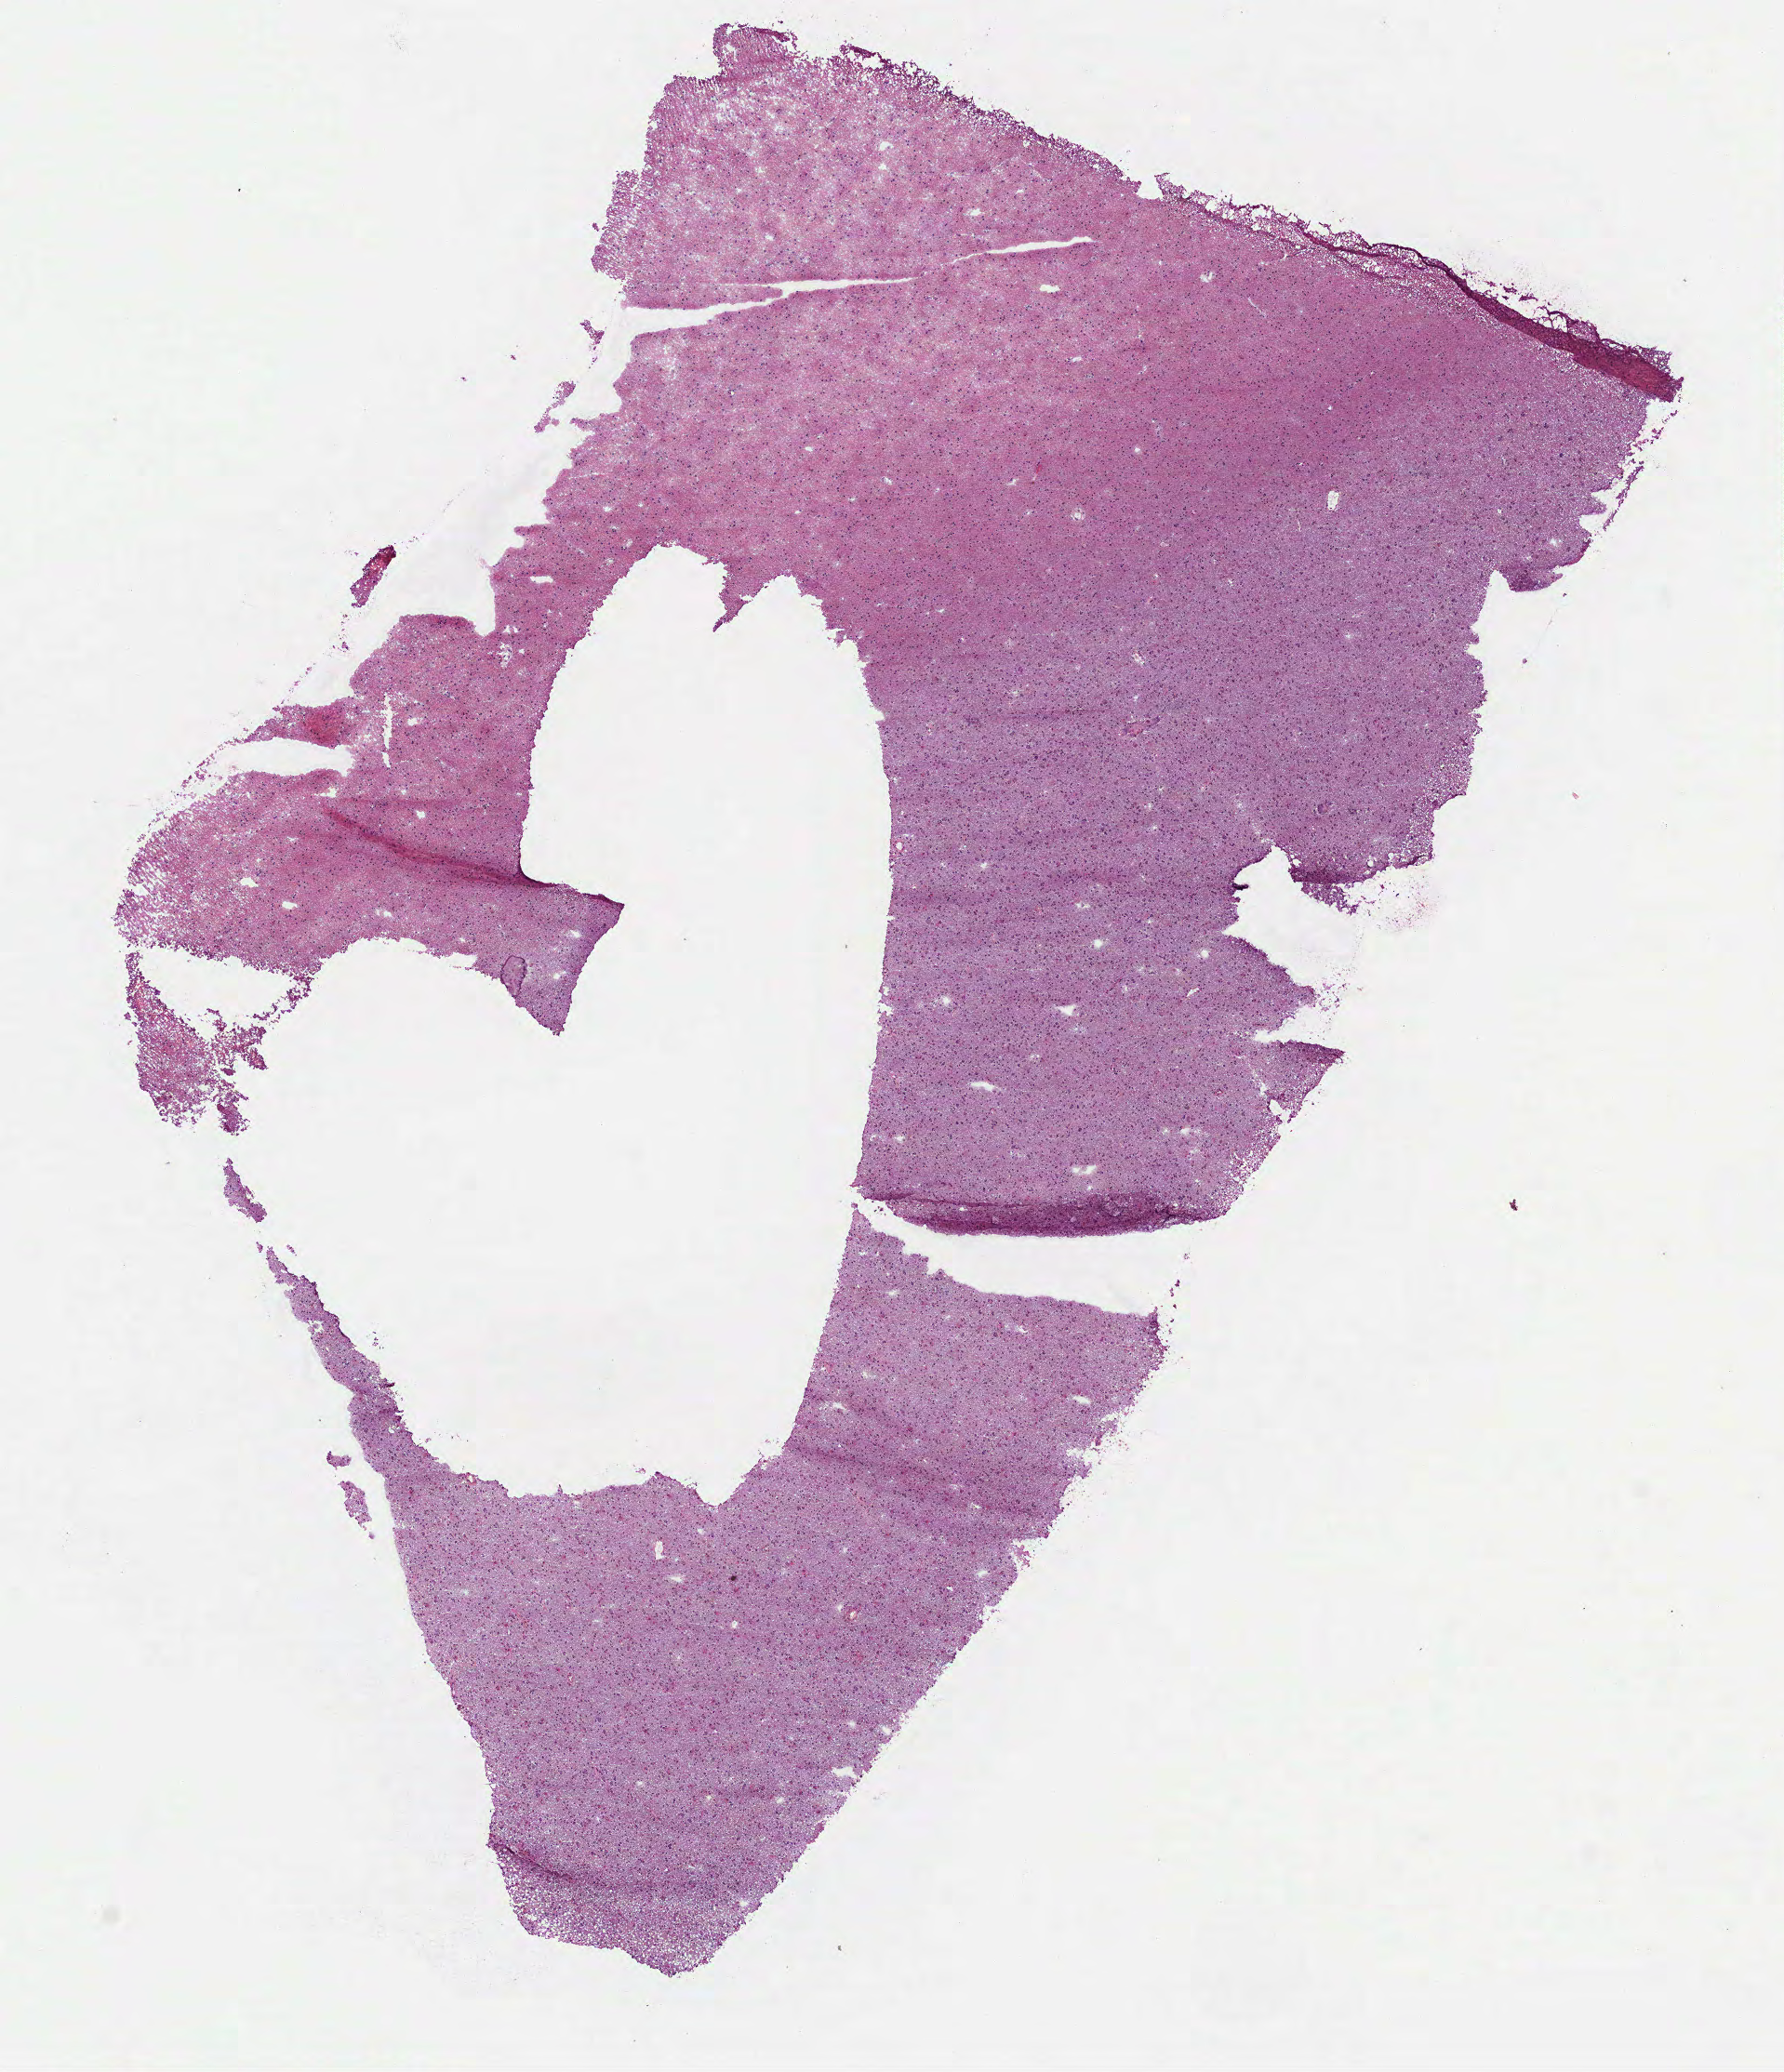
Hematoxylin and eosin (H&E) stained whole-slide image — low-resolution overview of the scanned area, about 7.7 x 9.0 mm (acquisition: 40x scan). Frozen section from the bottom of the tissue portion. Primary tumour sample from the brain. Male, age 69 years at initial diagnosis. Histologic grade: G3 (poorly differentiated). Pathologist review of this section (percent, as recorded): tumour cells 100%, tumour nuclei 60%, normal cells 0%, stromal cells 0%, necrosis 0%.
Pathologic diagnosis: Astrocytoma, anaplastic (cerebrum).